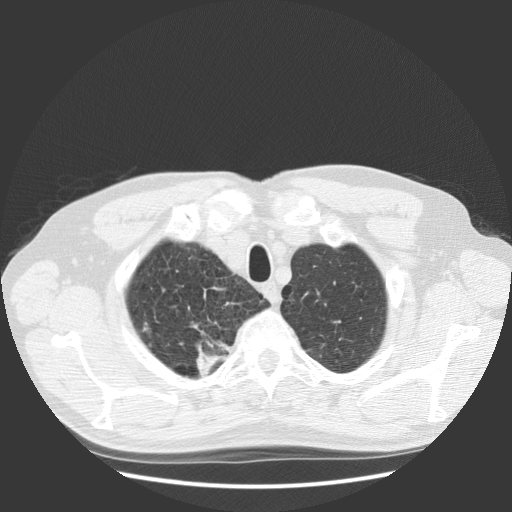
Chest CT (low-dose screening protocol), one axial image. Baseline annual screen. Lung window (W 1500 / L -600 HU). Slice 112 of 131 in the series. Male participant, aged 63 years at enrolment. Current smoker at enrolment.
Lesion marked by an expert reader, box from (x=171, y=325) to (x=243, y=386) px. The screening reader recorded 2 non-calcified nodules or masses ≥4 mm on this exam (right upper lobe, right upper lobe); which of them this box marks is not recorded. Lung cancer was diagnosed 30 days after this screen: squamous cell carcinoma, NOS, right upper lobe, stage IIIB (AJCC 6th edition), 35 mm at pathology.